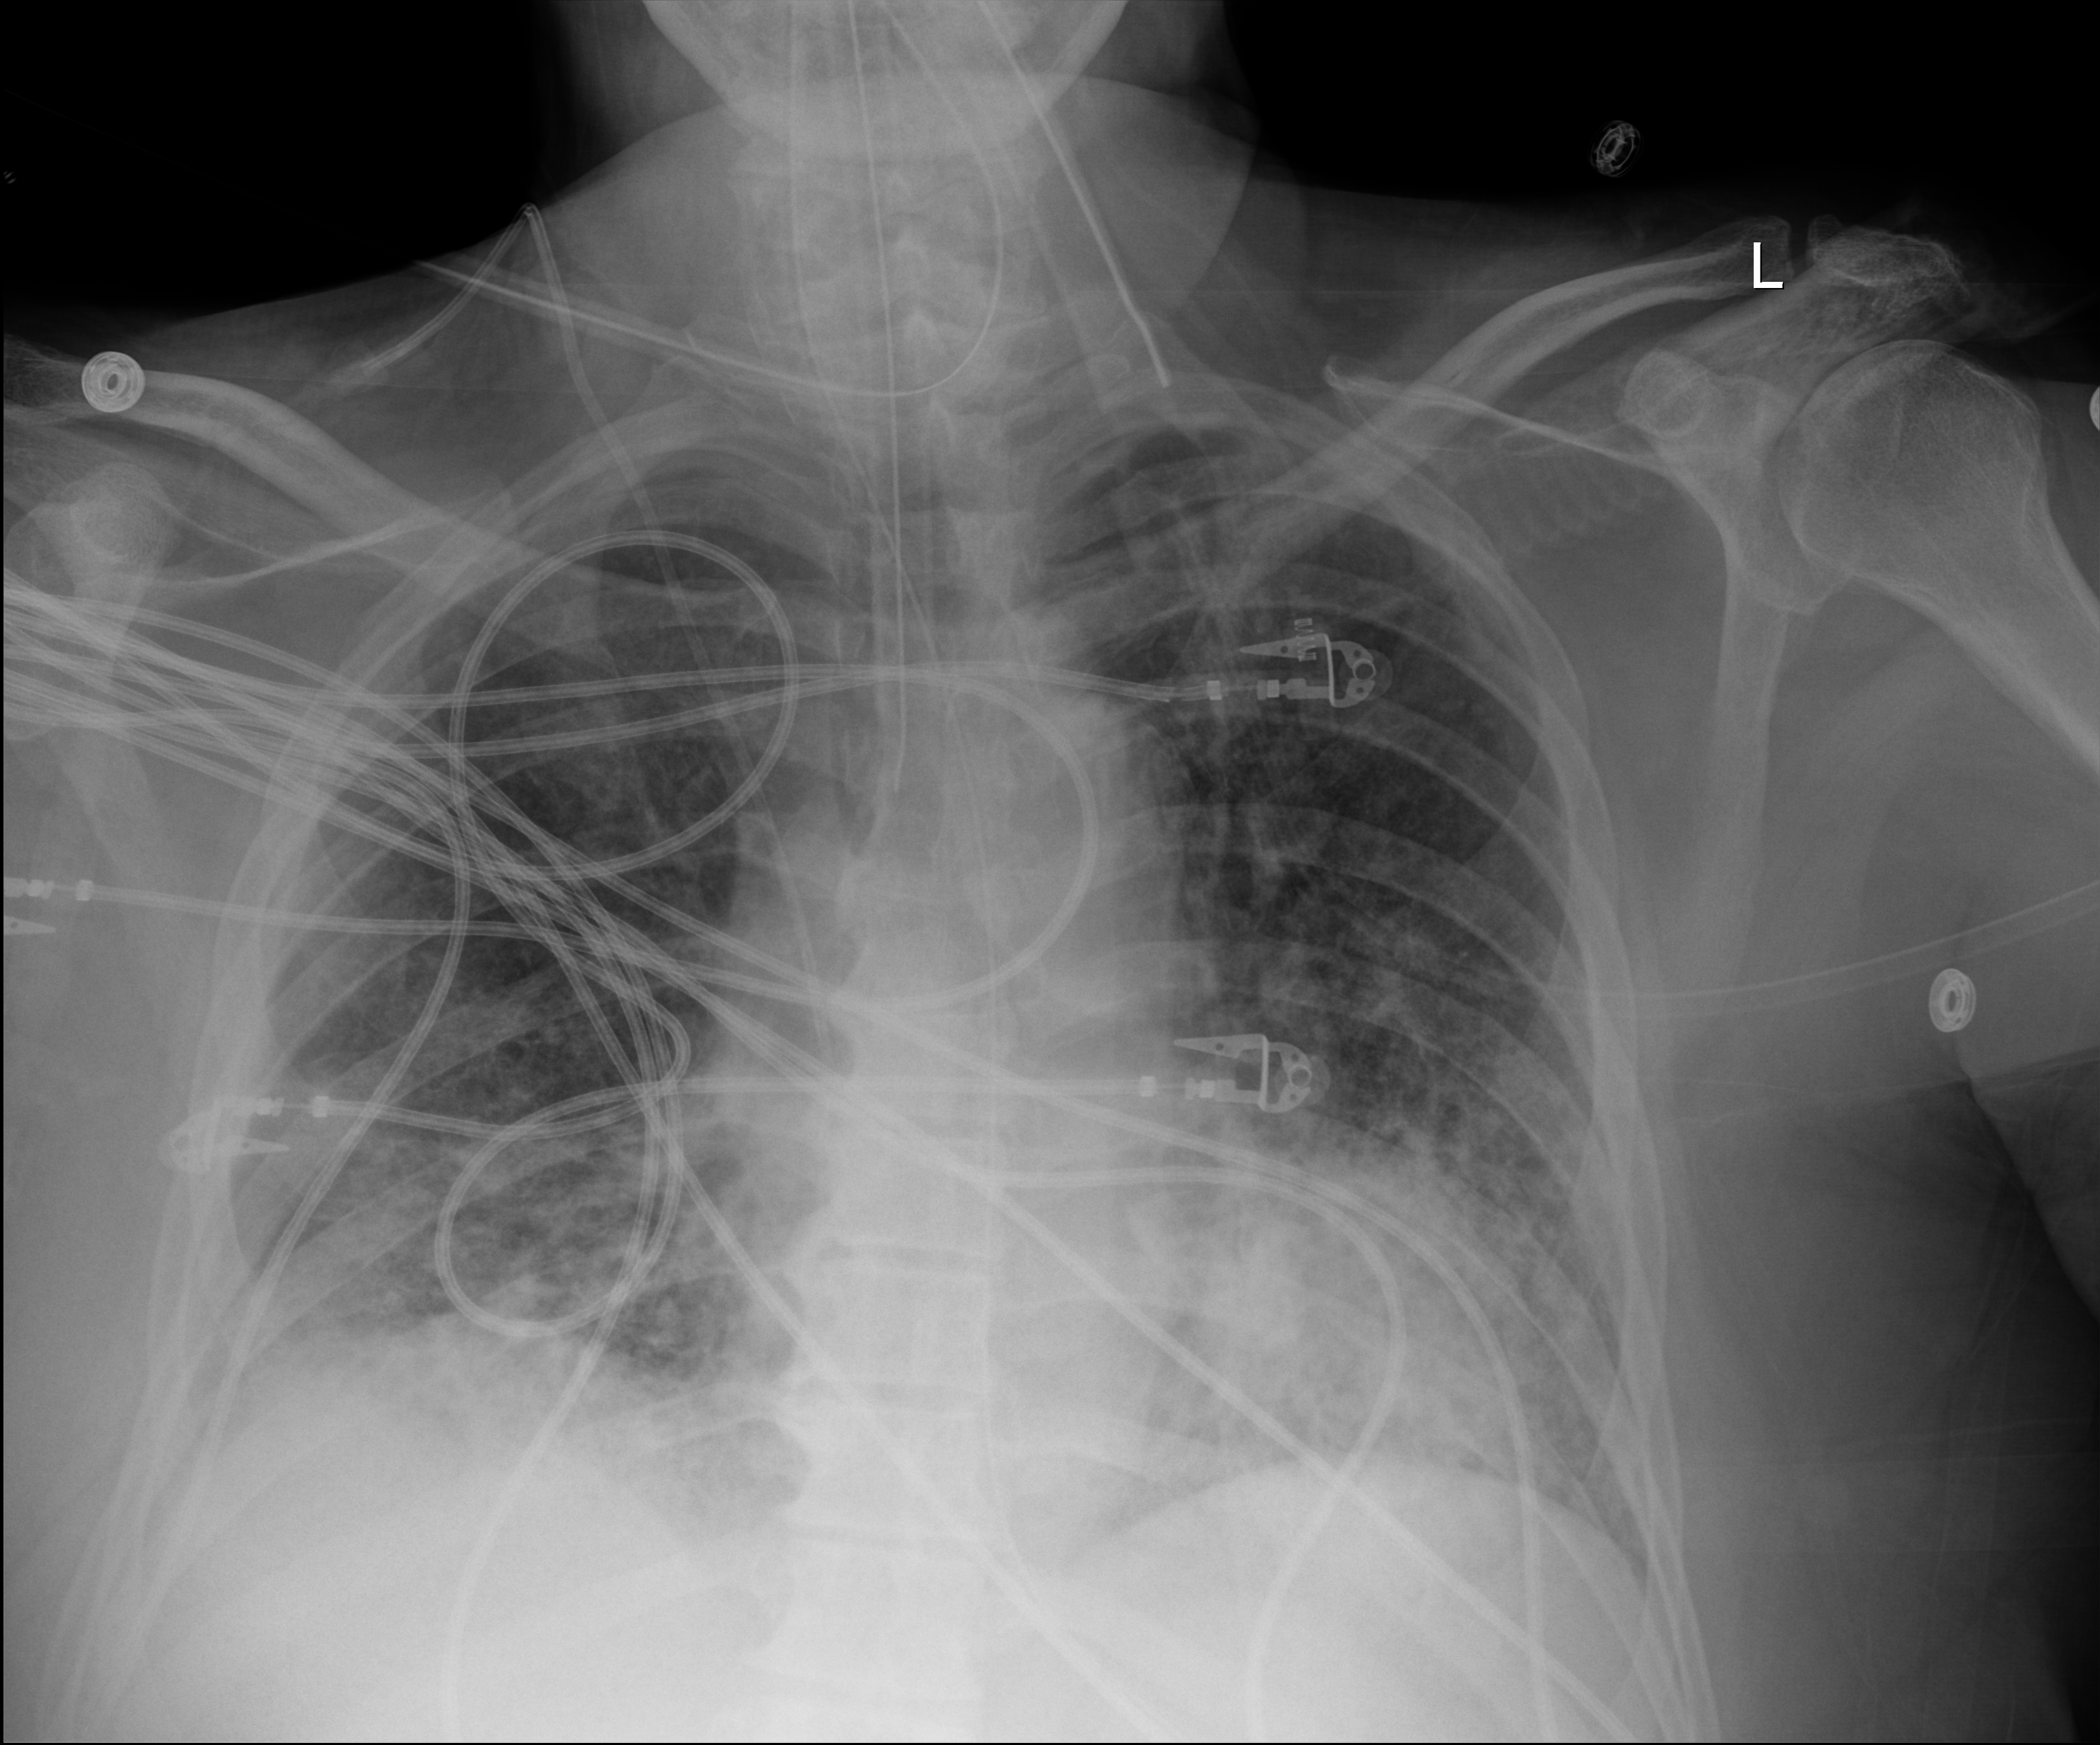
Portable chest radiograph. Patient hospitalised with COVID-19; male, aged 60–74 years.
Hospital-stay facts (about this admission, not read from this image; timing relative to this image not recorded):
- smoking status (admission record): former
- chronic kidney disease (admission record): no